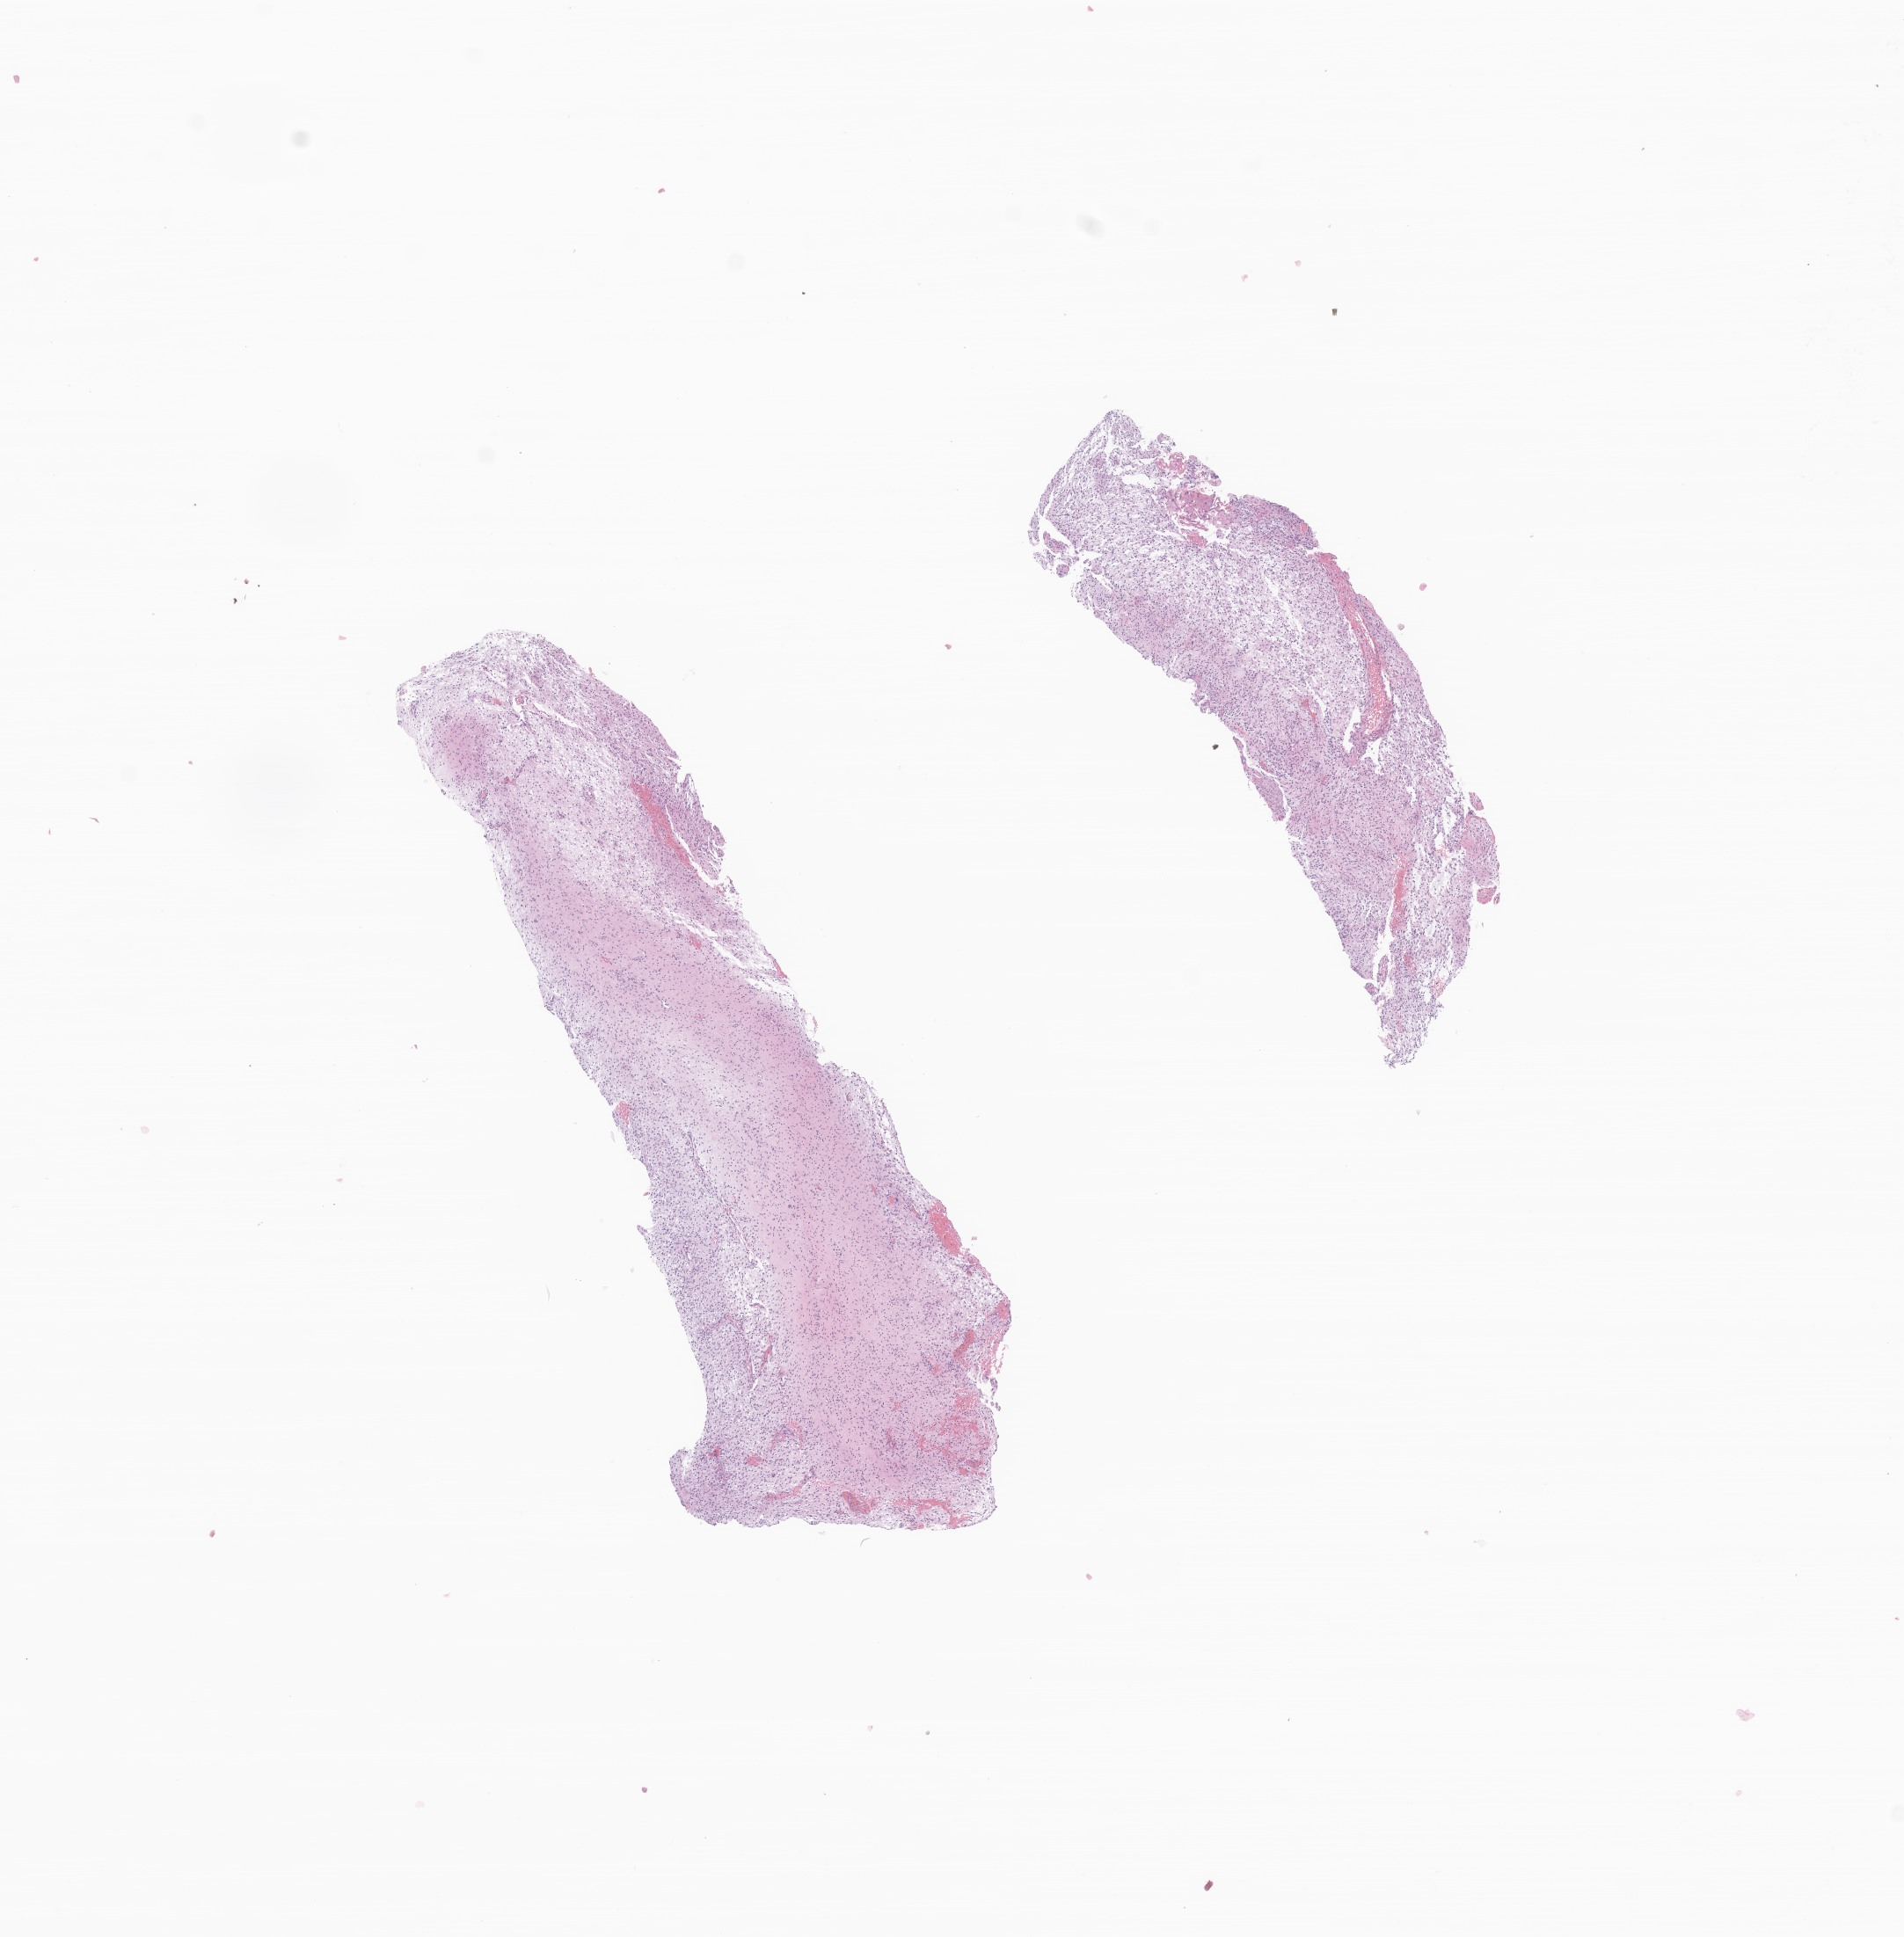
Digitized haematoxylin and eosin-stained section of tumor tissue from the brain, shown as a low-resolution overview of the whole scanned area (about 9.1 x 9.3 mm); FFPE section. Patient: female, age 711 days (about 1.9 years).
Diagnosis (ICD-O-3 morphology term): Pilocytic astrocytoma.